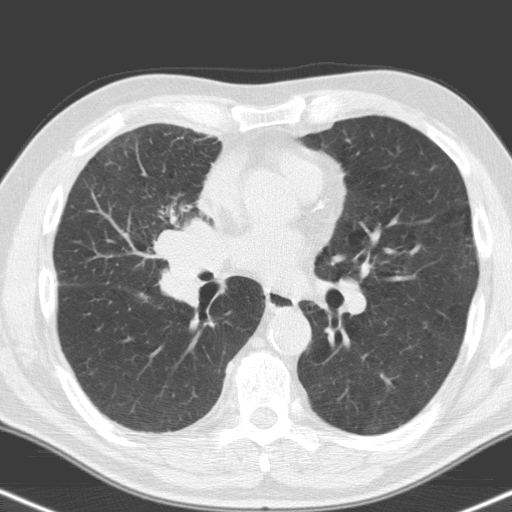
Low-dose screening chest CT, one axial slice; lung window (W 1500 / L -600 HU); 3.2 mm slice thickness; 512 × 512 image matrix, field of view 324 × 324 mm.
Structures marked on this image (expert manual segmentation):
- lesion 1 (tumor, hilum of right lung): bounding box <156,219,228,307> (left, top, right, bottom; pixels)